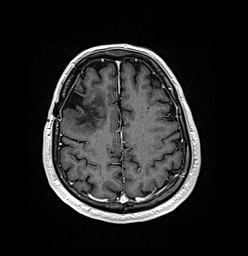
Brain MRI from a brain-tumour surgery series, one axial slice; slice 47 of 176 in the series (ordered by position); T1-weighted post-contrast; 248 × 256 image matrix. From the clinical record (not read from this slice): histopathology: Oligodendroglioma; WHO grade: 3; IDH mutation: yes; tumour location: Right Frontal.
Annotated regions visible in this slice (expert manual segmentation):
- previous resection cavity: bounding box (x1, y1, x2, y2) in pixels: (63, 87, 84, 109)